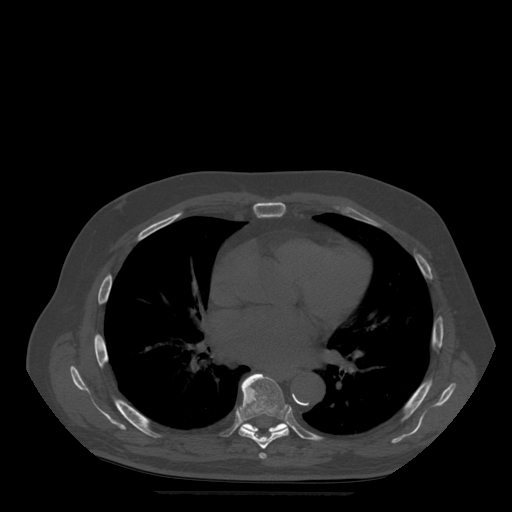
CT including the spine, one axial slice; slice 327 of 522 in the series (ordered by position); bone window (W 1800 / L 400 HU); 512 × 512 image matrix, field of view 420 × 420 mm. Patient age 72 years. From the clinical record (not read from this slice): primary cancer: prostate.
Structures marked on this image (semi-automatic segmentation, software-assisted and operator-edited):
- T6 vertebra: bounding box (x1, y1, x2, y2) in pixels: (259, 453, 267, 459)
- T7 vertebra: (238, 374, 289, 449)
- T8 vertebra: (241, 382, 288, 432)